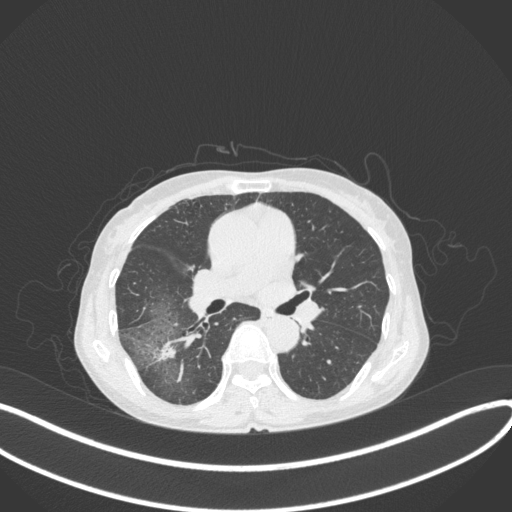
Chest CT, one axial slice. Position 220 of 379 along the scan axis. 120 kVp. Lung window (W 1500 / L -600 HU). 1 mm slice thickness. 512 × 512 image matrix, field of view 400 × 400 mm. Patient: female, 69 years. From the clinical record (not read from this slice): clinical TNM (as recorded): T1b N0 M0; histopathological grade: G2-3.
Structures marked on this image (bounding box drawn by a radiologist):
- lung tumour (recorded histology: adenocarcinoma): bounding box <150,340,181,365> (left, top, right, bottom; pixels)